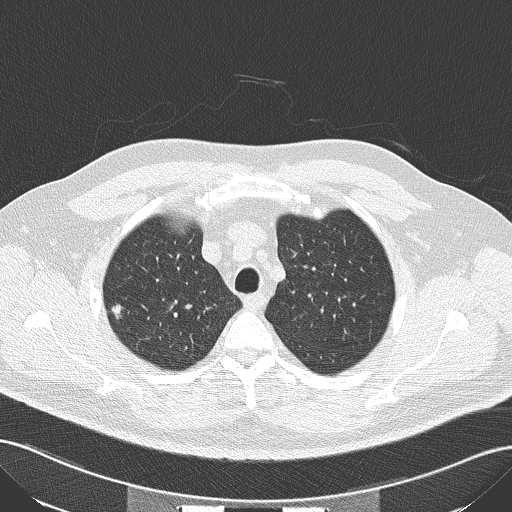
Axial slice from a low-dose chest CT screening exam. Second annual screen. Lung window (W 1500 / L -600 HU). 2 mm slice thickness. Lung (sharp) reconstruction kernel (B50f). 512 × 512 image matrix, field of view 360 × 360 mm. Male participant, aged 56 years at enrolment.
- Expert reader's lesion annotation, bounding box (x1, y1, x2, y2) in pixels: (96, 293, 142, 331).
- The exam's reader record, not a measurement of the box and not confirmed to be the same lesion: non-calcified nodule or mass ≥4 mm, right upper lobe, 10 × 9 mm, spiculated (stellate) margins, soft tissue attenuation, pre-existing on the prior screen: no.
- Official screen result: positive, other.
- Lung cancer was diagnosed 117 days after this screen: squamous cell carcinoma, NOS, right upper lobe, moderately differentiated (G2), stage IA (AJCC 6th edition), 10 mm at pathology.